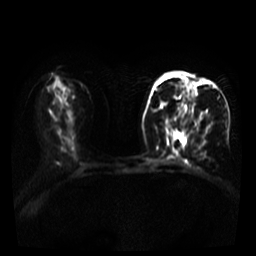
Breast MRI, one axial slice. Position 14 of 39 along the scan axis. Diffusion-weighted series; image 2 of 4 stored at this slice position (different b-values; order by instance number). 3 T. 5 mm slice thickness. 256 × 256 image matrix, field of view 320 × 320 mm. Female patient.
Structures marked on this image (manually delineated by an expert):
- tumour on diffusion-weighted imaging: bounding box (x1, y1, x2, y2) in pixels: (160, 86, 196, 108)